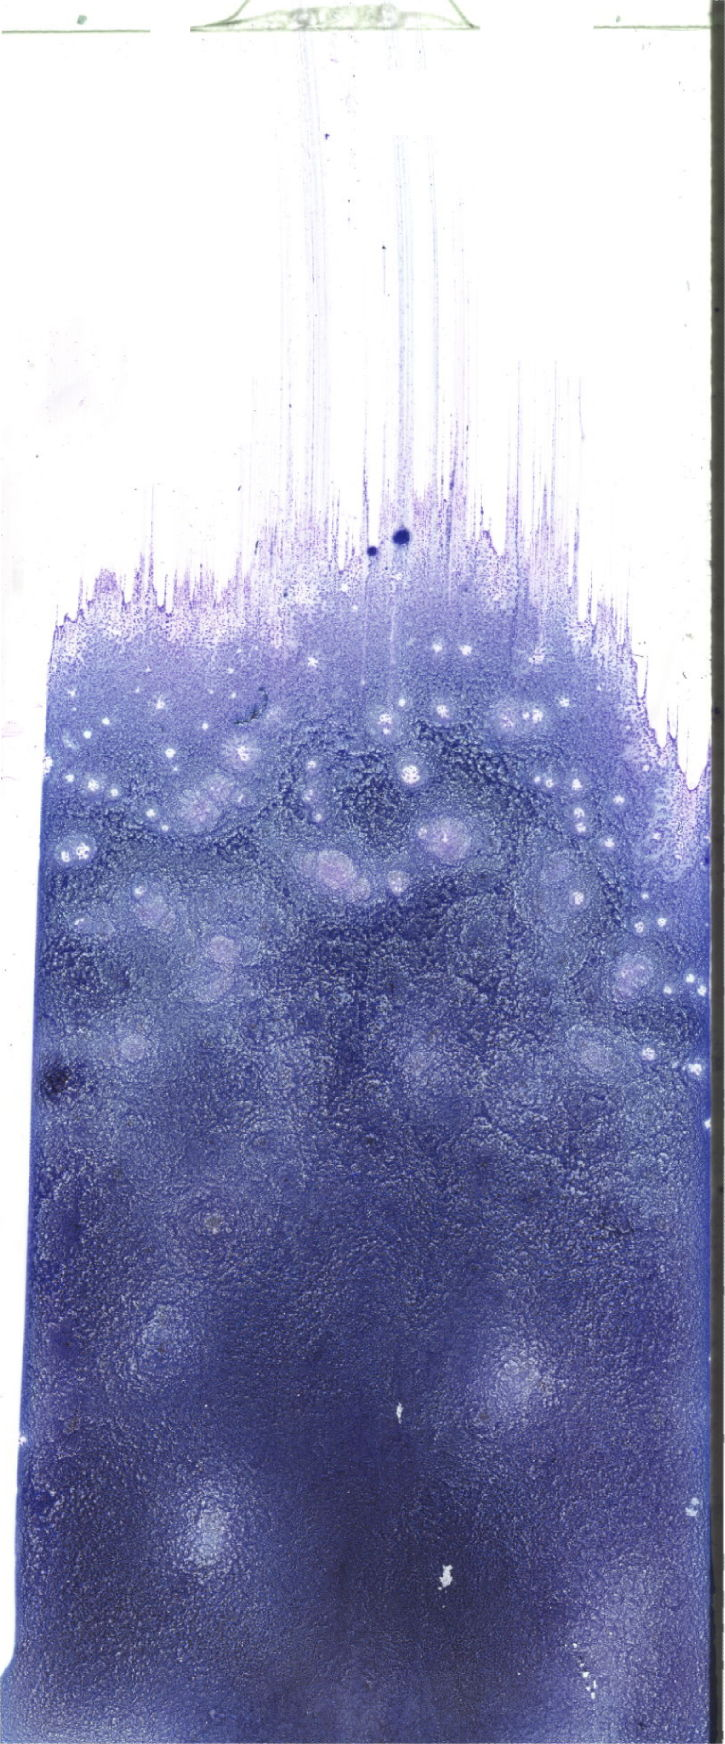
Bone marrow aspirate smear, May-Grünwald–Giemsa stain, whole-slide image, shown as a low-resolution overview of the whole scanned area (about 20.6 x 49.4 mm). Patient sex: female.
Diagnosis: Acute Myelomonocytic Leukemia with Abnormal Eosinophils.